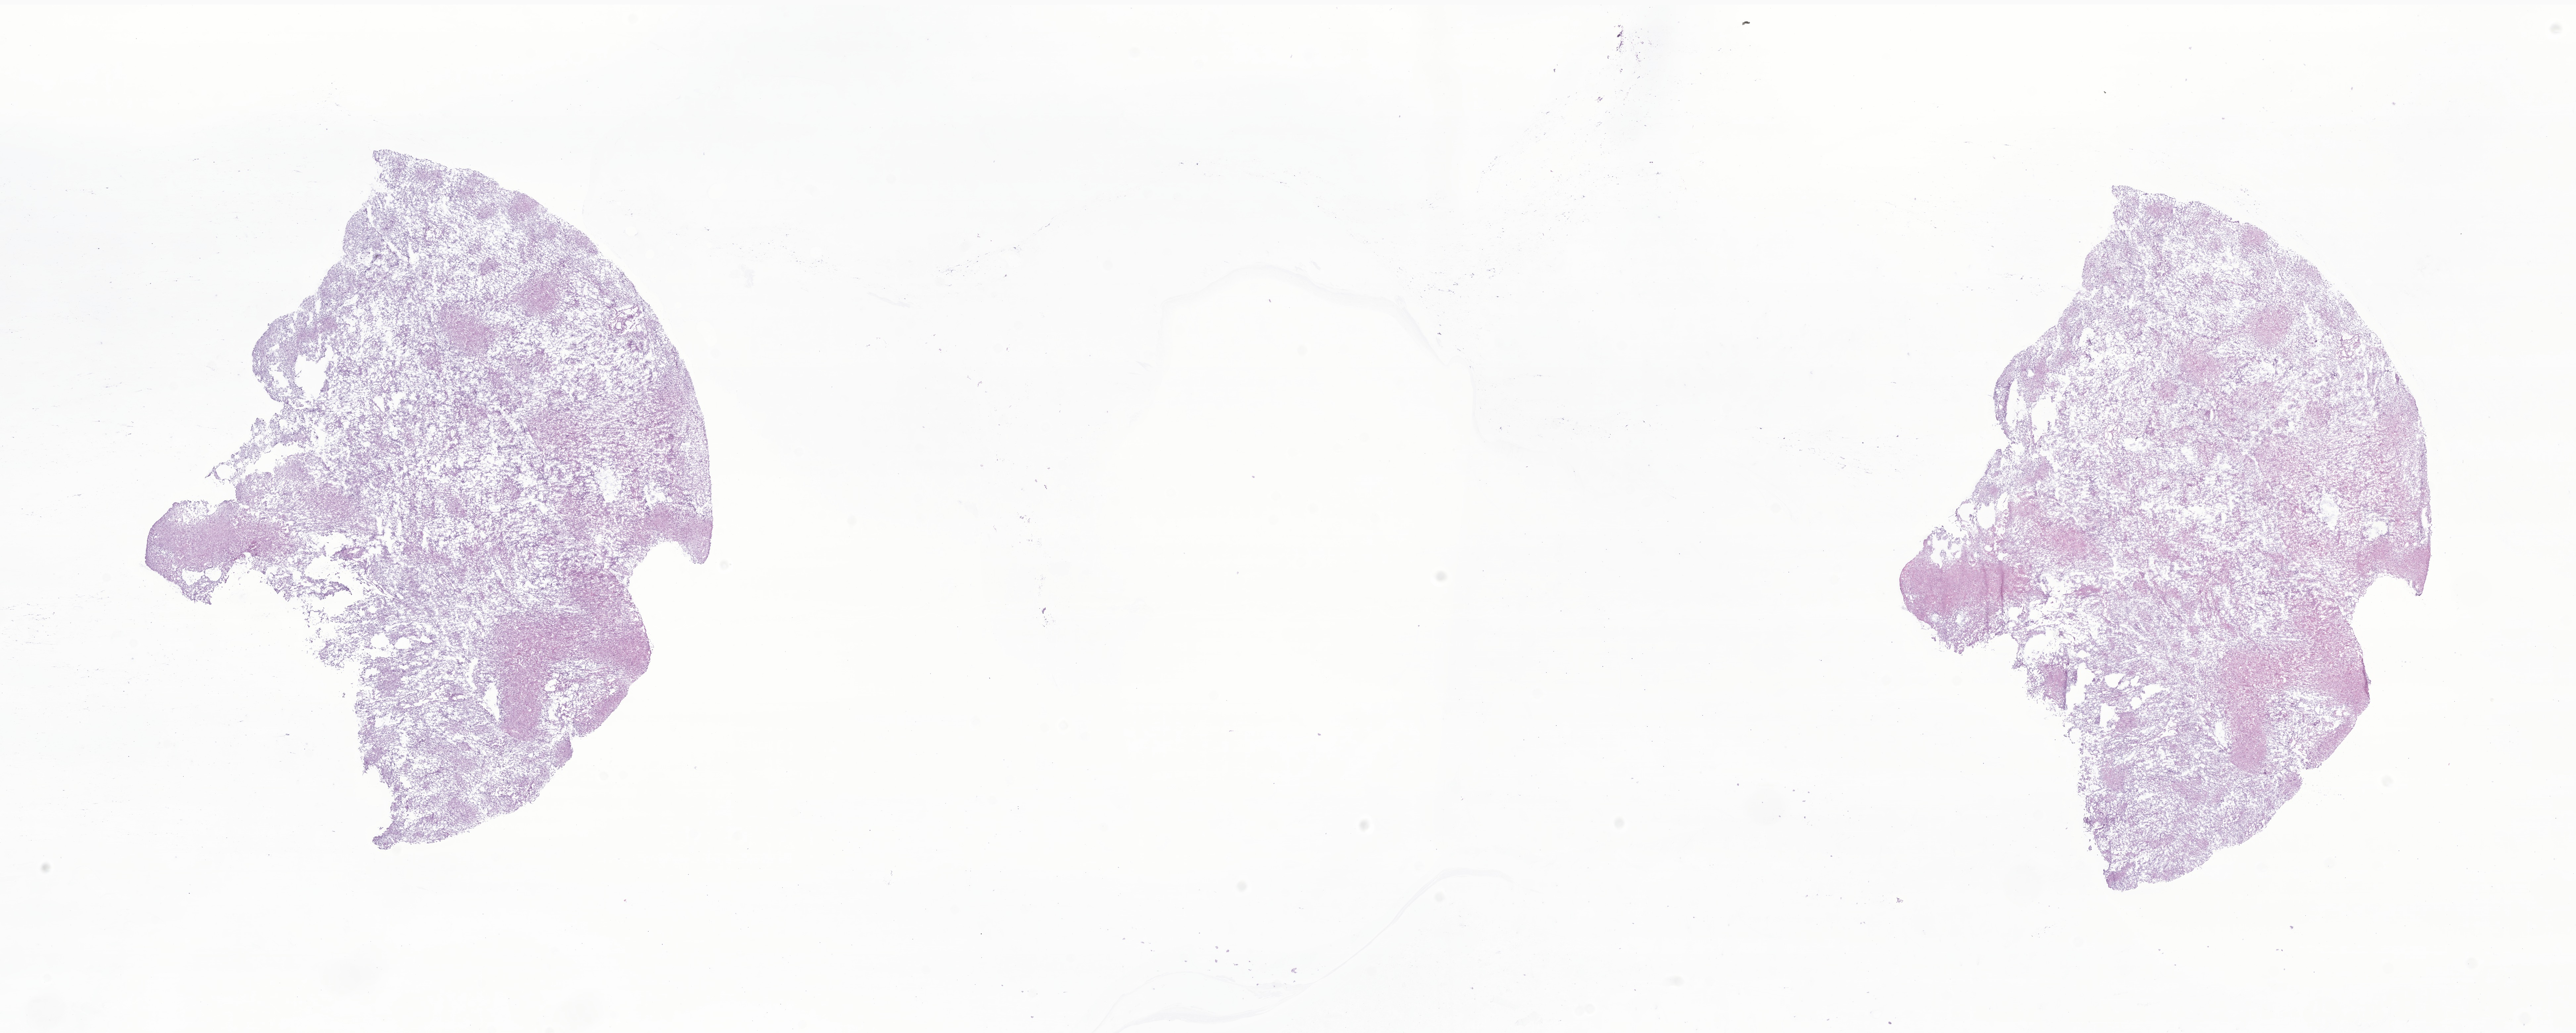
Whole-slide image, H&E stain of tumor tissue from the brain, shown as a low-resolution overview of the whole scanned area (about 32.8 x 13.2 mm), frozen section (OCT-embedded). Male patient, age 56 months (4 years 8 months).
Recorded diagnosis: Hemangioblastoma.